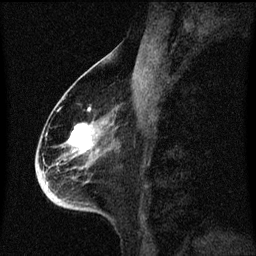
Breast MRI (dynamic contrast-enhanced), one sagittal slice. Position 31 of 60 along the scan axis. Dynamic contrast-enhanced series, image 2 of 3 at this slice position (ordered by acquisition). 1.5 T. TE 4.2 ms, TR 8.4 ms. 2 mm slice thickness. 256 × 256 image matrix, field of view 200 × 200 mm. Patient: female, 68 years. From the clinical record (not read from this slice): setting: breast cancer imaged before/during neoadjuvant chemotherapy; receptor status: triple-negative.
Structures marked on this image (semi-automatic segmentation, software-assisted and operator-edited):
- analysis volume of interest (the breast-tissue region the enhancement analysis was run in; not a lesion): box from (x=38, y=96) to (x=113, y=213) px
- tumour enhancement mask (voxels above the 70 % enhancement threshold inside the analysis volume of interest): (x=69, y=124)–(x=94, y=155)